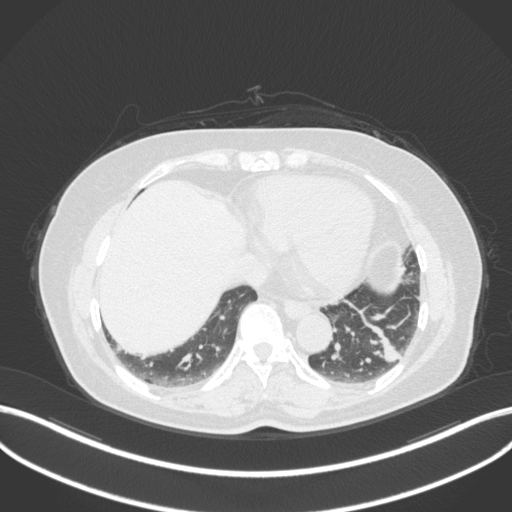
Chest CT, one axial slice. Position 114 of 307 along the scan axis. Lung window (W 1500 / L -600 HU). 1 mm slice thickness. 512 × 512 image matrix, field of view 400 × 400 mm. Patient: female, 59 years. Case-level facts recorded for this patient, not image findings: clinical TNM (as recorded): T2a N0 M0; histopathological grade: G2-3.
Annotated regions visible in this slice (bounding box drawn by a radiologist):
- lung tumour (recorded histology: adenocarcinoma): bounding box <366,322,403,367> (left, top, right, bottom; pixels)